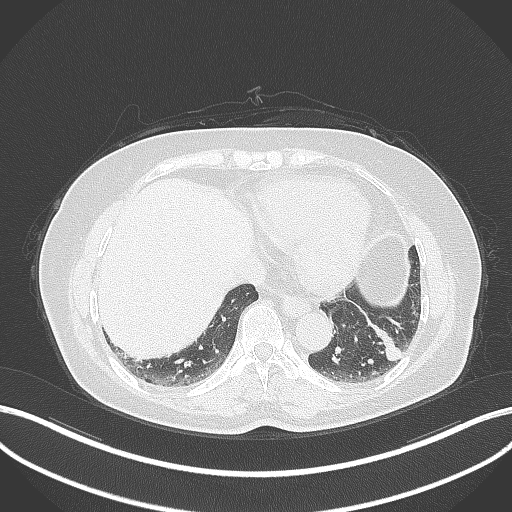
Chest CT, one axial slice; position 109 of 311 along the scan axis; reconstruction kernel B70f; lung window (W 1500 / L -600 HU); 1 mm slice thickness; 512 × 512 image matrix, field of view 400 × 400 mm. Female patient, age 59 years. Case-level facts recorded for this patient, not image findings: clinical TNM (as recorded): T2a N0 M0.
Annotated regions visible in this slice (rectangle marked by the reading radiologist):
- lung tumour (recorded histology: adenocarcinoma): bounding box (x1, y1, x2, y2) in pixels: (365, 321, 405, 364)